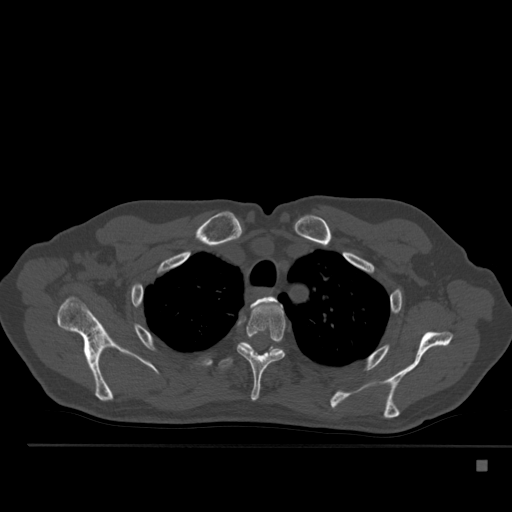
CT including the spine, one axial slice. Slice 395 of 517 in the series (ordered by position). 120 kVp. Bone window (W 1800 / L 400 HU). 1.5 mm slice thickness. 512 × 512 image matrix, field of view 408 × 408 mm. Patient: male, 70 years. From the clinical record (not read from this slice): primary cancer: renal; vertebrae with lytic lesions (as recorded): T4, T6, T10, T12, L3, L4, L5.
Structures marked on this image (semi-automatically segmented with operator editing):
- T2 vertebra: box from (x=252, y=296) to (x=278, y=306) px
- T3 vertebra: (x=237, y=304)–(x=285, y=401)
- T4 vertebra: (x=219, y=342)–(x=281, y=370)